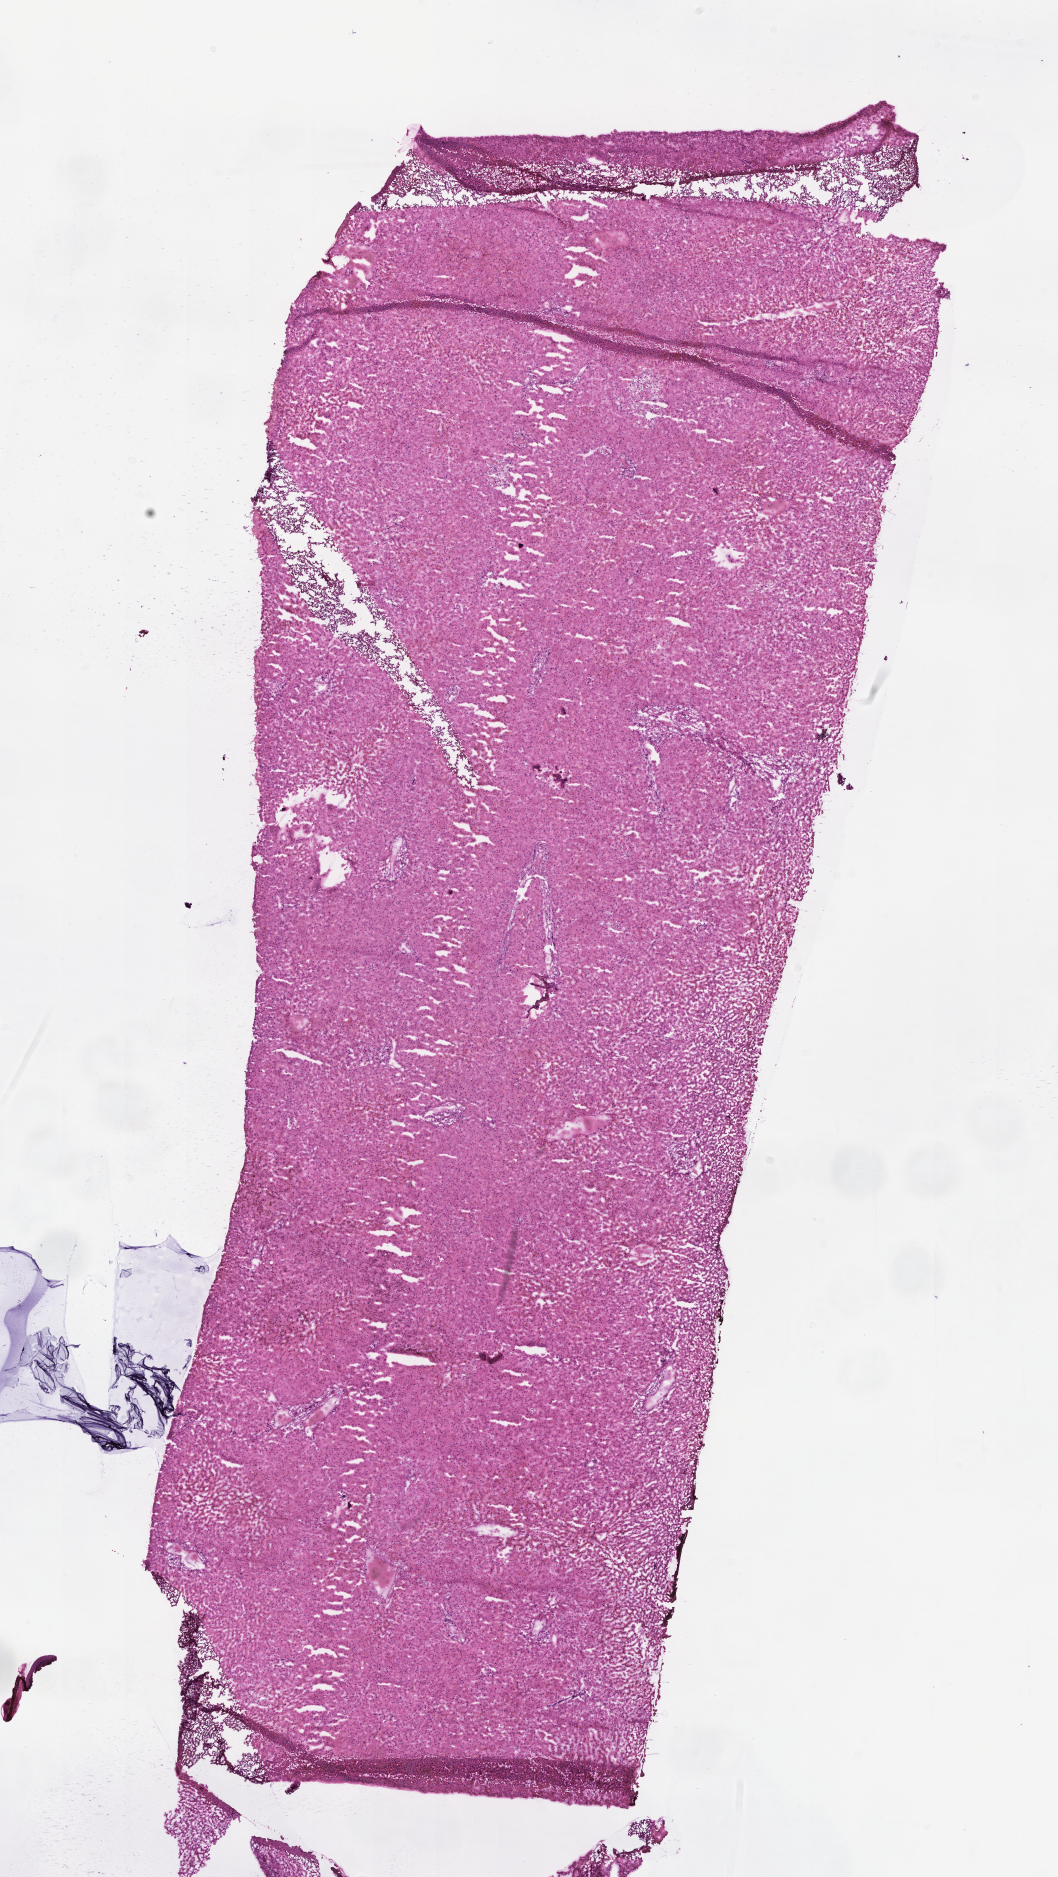
Hematoxylin and eosin (H&E) whole-slide image — whole scanned area (about 8.6 x 15.2 mm) shown as a low-resolution overview. Frozen section (tissue freezing medium). Non-tumor (normal tissue) sample from a patient with adenocarcinoma, NOS. Site: colon. Patient: male, age at initial diagnosis 84 years. Composition of this section per pathologist review: tumor cells 0%, tumor nuclei 0%, stromal cells 0%, necrosis 0%, normal cells 100%. Inflammatory infiltration, as recorded: lymphocyte infiltration 5%, monocyte infiltration 0%, neutrophil infiltration 0%.
- this section: non-tumor tissue sample; the patient's diagnosis is given above
- section: bottom of the tissue portion